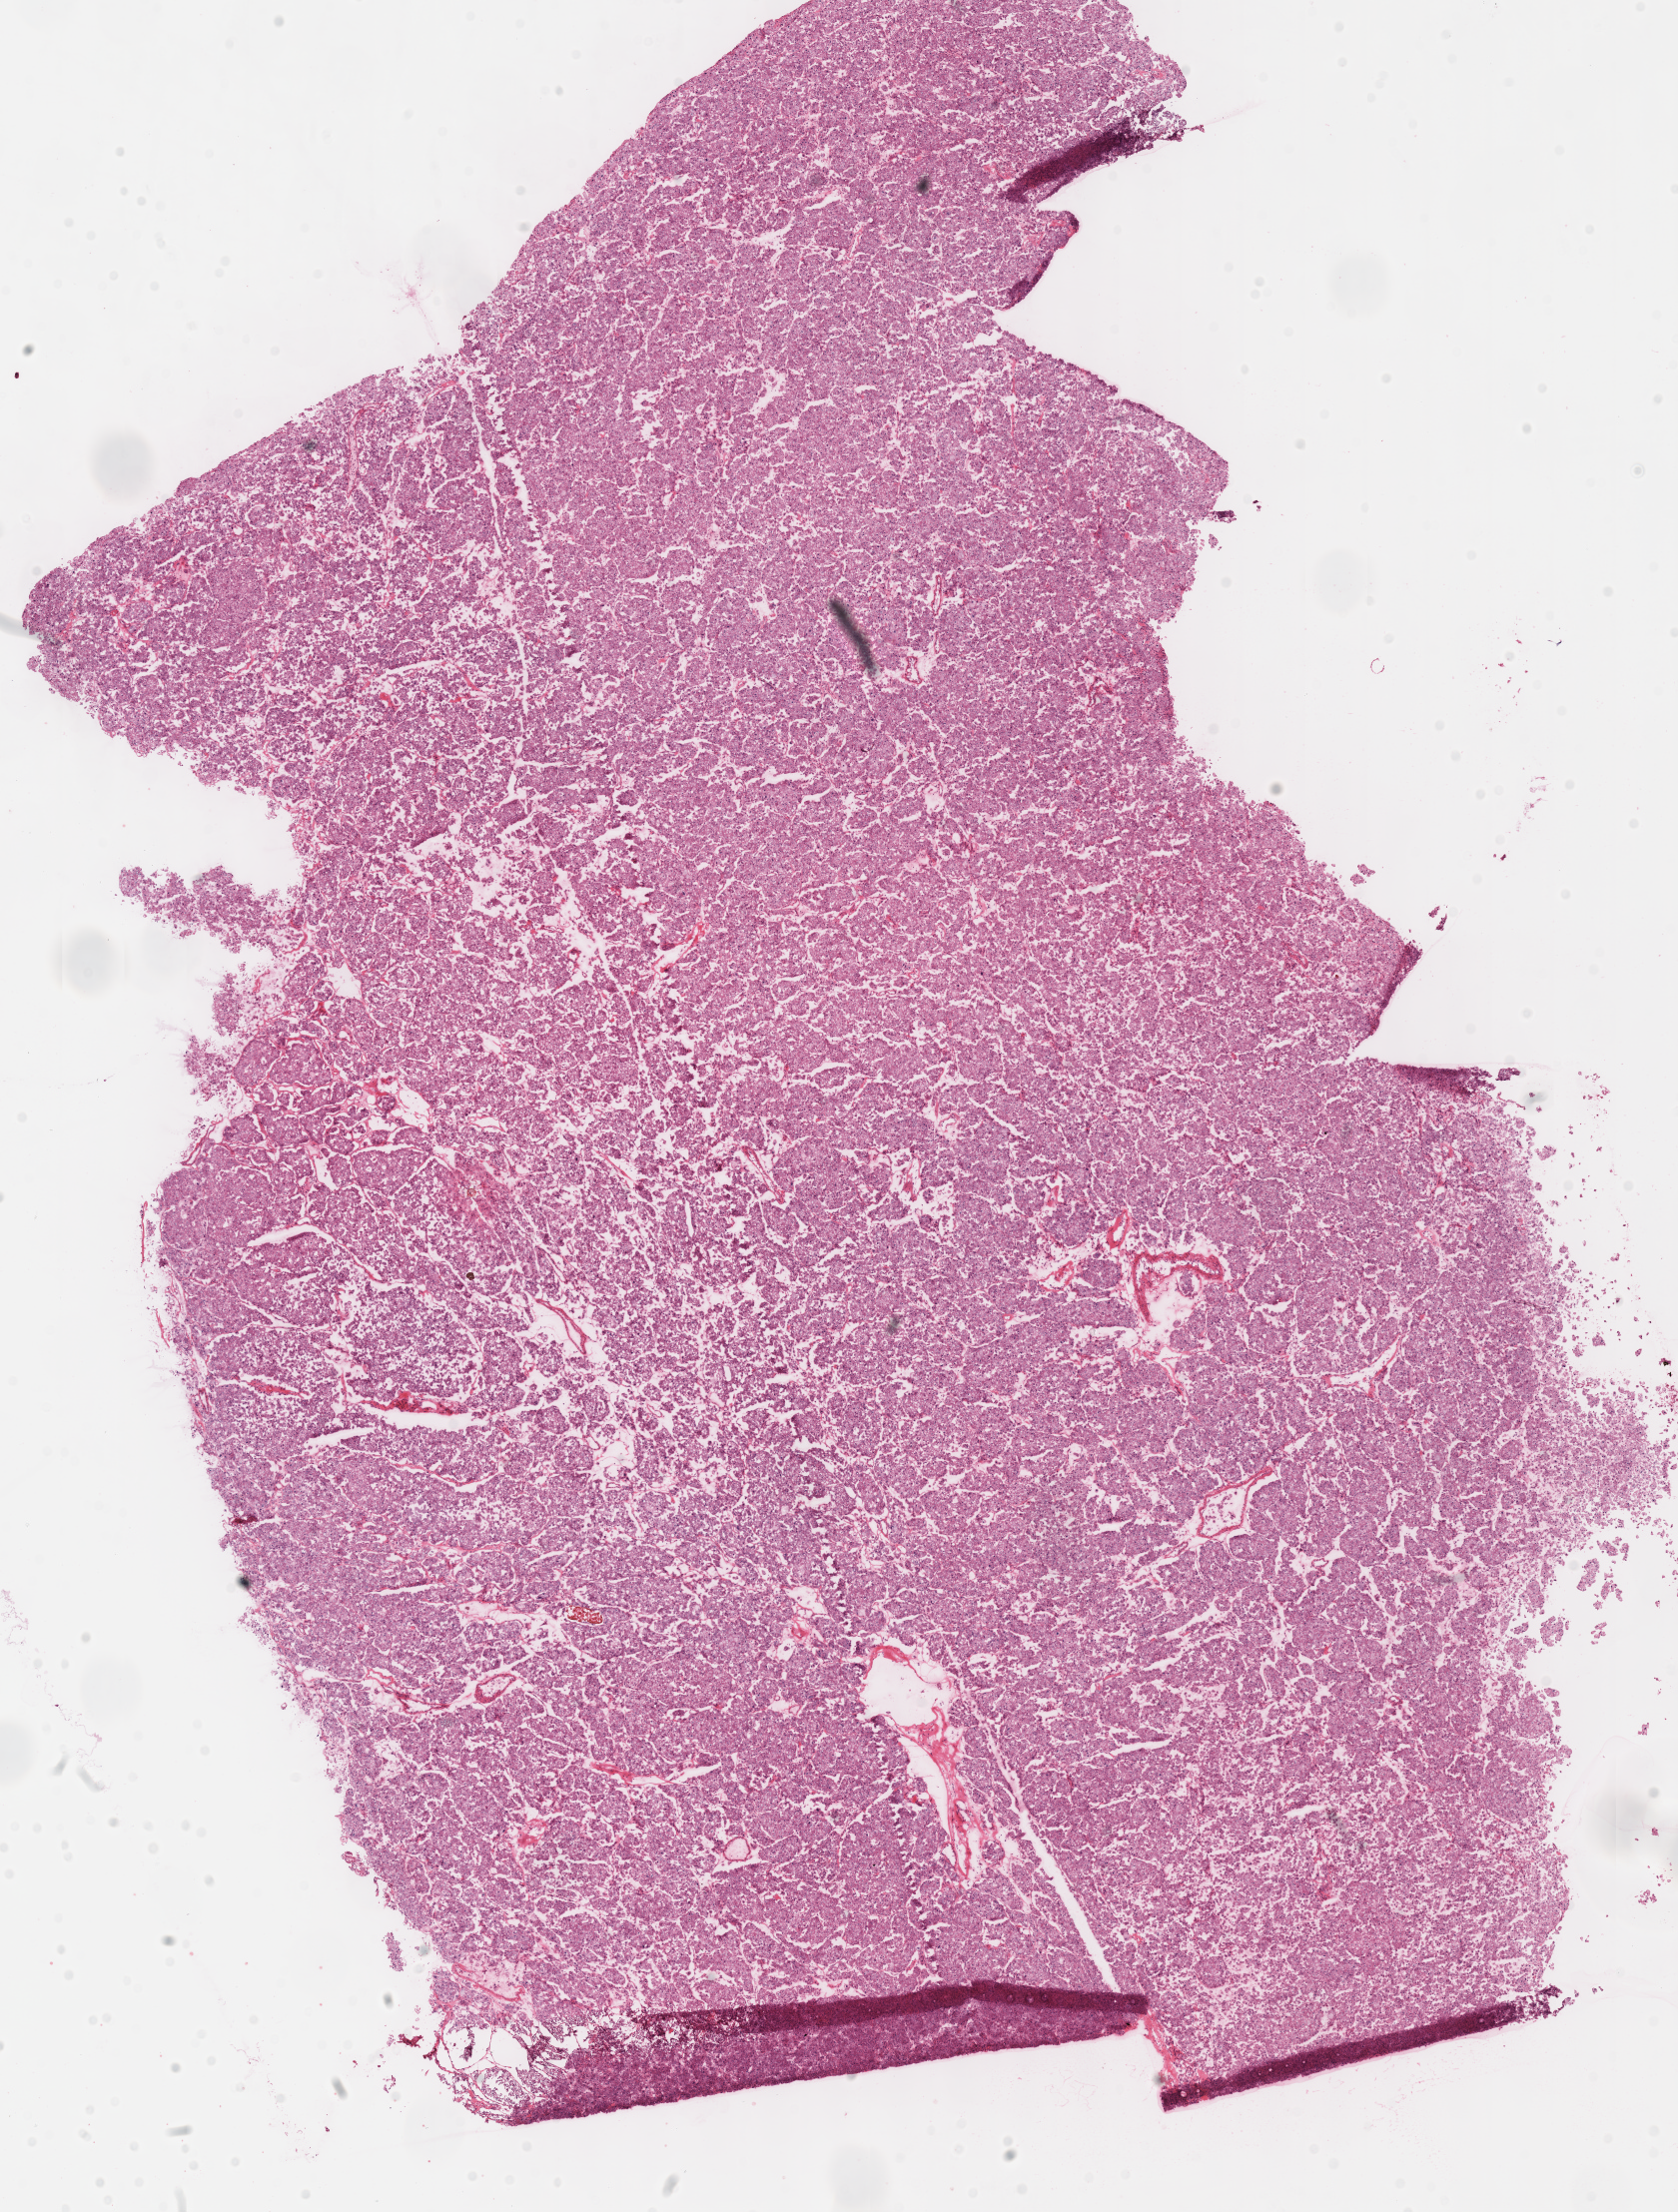
Whole-slide histology image, Hematoxylin and eosin (H&E) stained — shown as a low-resolution overview of the whole scanned area (about 13.2 x 17.4 mm, slide scanned at 40x), frozen section, primary tumour sample from the kidney. Male patient; age at initial diagnosis 55 years. Pathologist review of this section (percent, as recorded): tumour cells 100%, tumour nuclei 95%, normal cells 0%, stromal cells 0%, necrosis 0%. Infiltration values recorded for this section: lymphocyte infiltration 1%, monocyte infiltration 0%, neutrophil infiltration 0%.
Histologic diagnosis: Renal cell carcinoma, chromophobe type. Lymph nodes positive (case pathology): 0 of 1 examined. Laterality: right. AJCC pathologic stage: I.